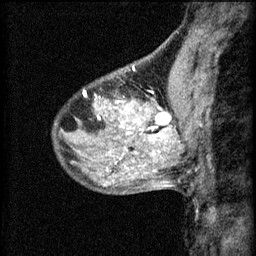
Breast MRI (dynamic contrast-enhanced), one sagittal slice; slice 24 of 60 in the series (ordered by position); 3 images stored at this slice position (order not interpretable as contrast timing); 1.5 T; TE 4.2 ms, TR 8.2 ms; 256 × 256 image matrix. Female patient, age 40 years.
Outlined on this slice (semi-automatically segmented with operator editing):
- analysis volume of interest (the breast-tissue region the enhancement analysis was run in; not a lesion): bounding box (x1, y1, x2, y2) in pixels: (108, 82, 175, 139)
- tumour enhancement mask (voxels above the 70 % enhancement threshold inside the analysis volume of interest): (116, 94, 171, 135)